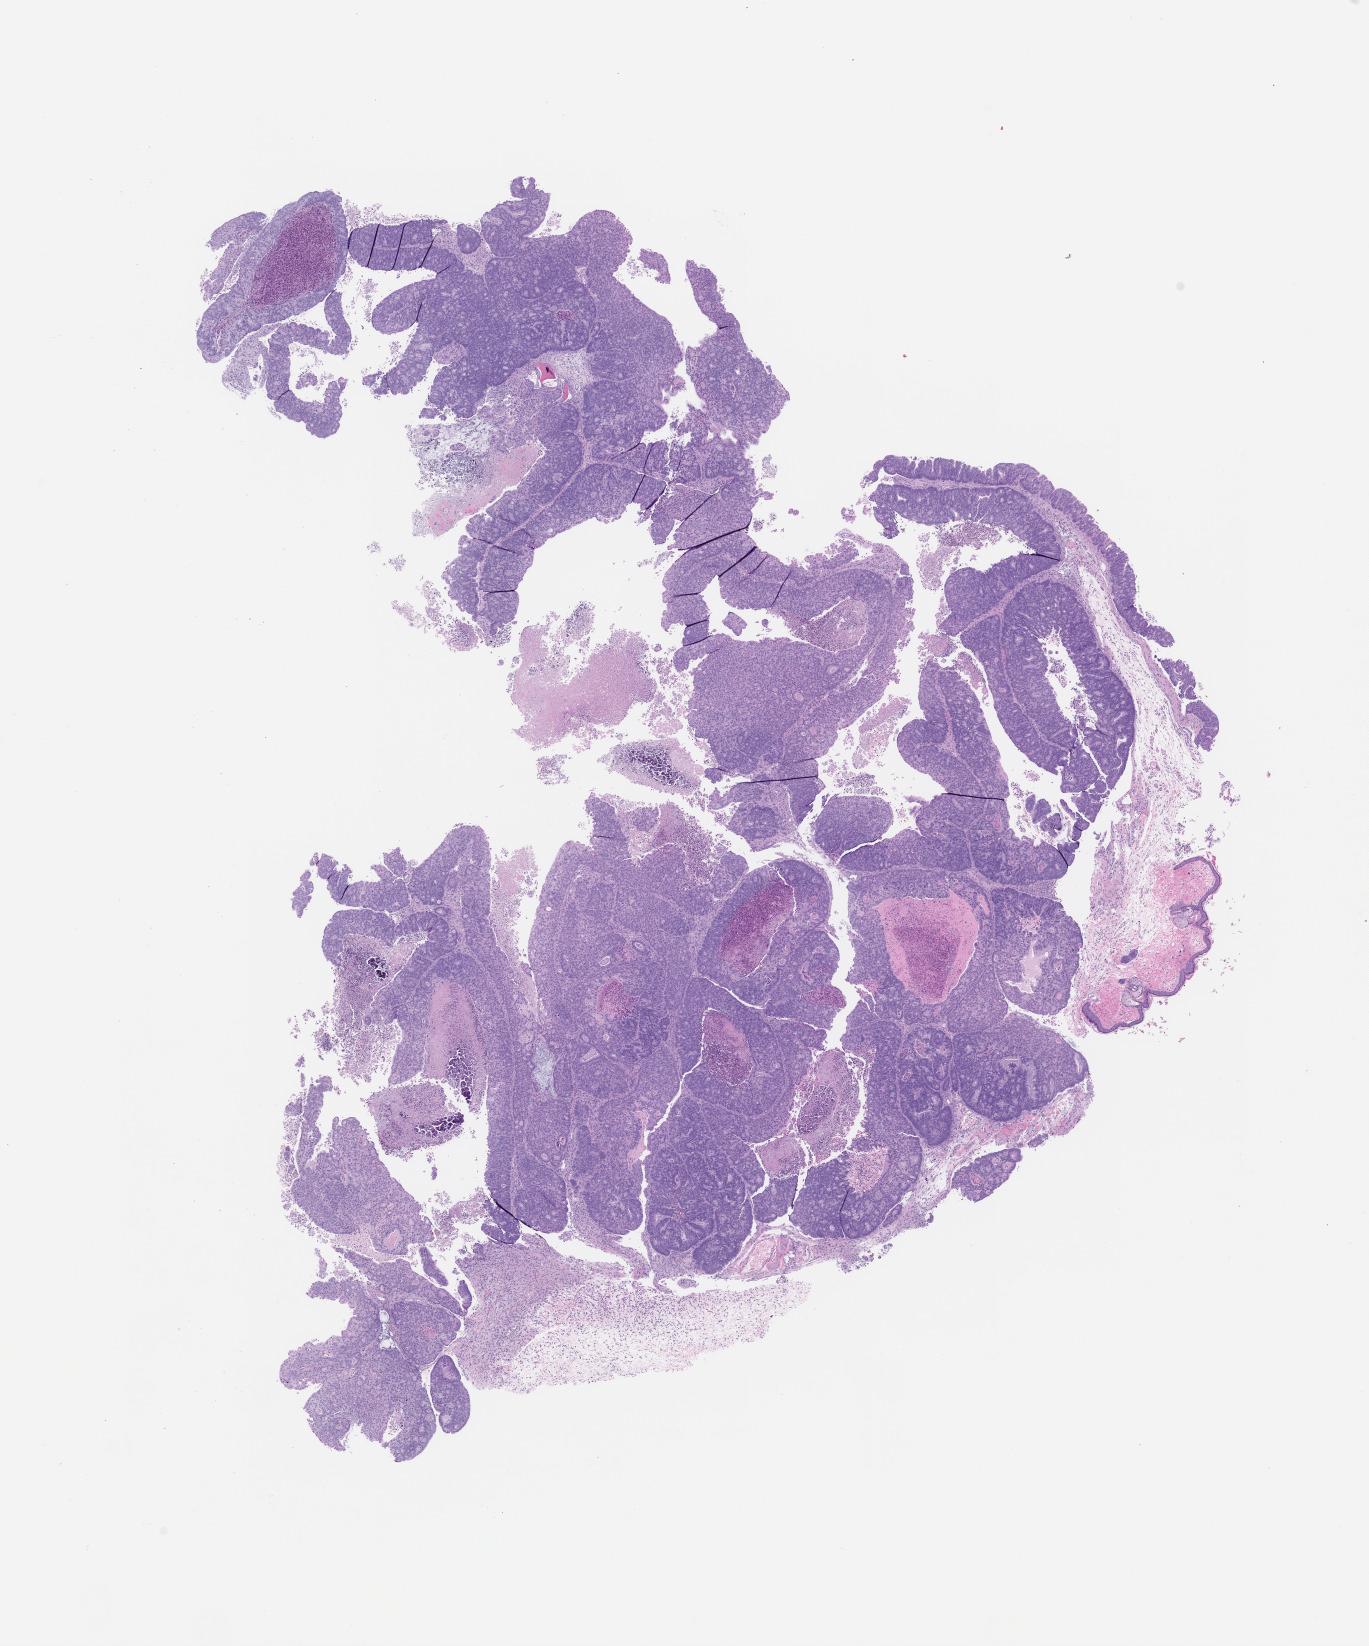
Hematoxylin and eosin (H&E) whole-slide image of a patient-derived xenograft (PDX) tumor grown in a mouse, passage 1, low-resolution overview of the scanned area, about 11.0 x 13.2 mm. FFPE section. Tumor site category: colon.
Originating patient diagnosis: Colon Adenocarcinoma.